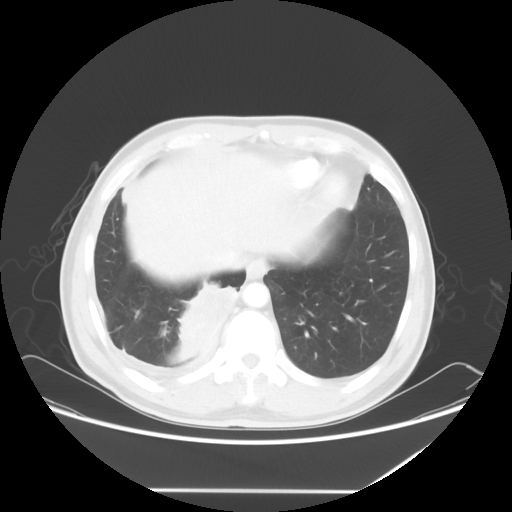
Chest CT, one axial slice; slice 14 of 60 in the series (ordered by position); 120 kVp; lung window (W 1500 / L -600 HU); 5 mm slice thickness; 512 × 512 image matrix, field of view 419 × 419 mm. Patient: male, 48 years. From the clinical record (not read from this slice): clinical TNM (as recorded): T3 N3 M1a.
Outlined on this slice (rectangle marked by the reading radiologist):
- lung tumour (recorded histology: squamous cell carcinoma): bounding box (x1, y1, x2, y2) in pixels: (169, 274, 242, 361)